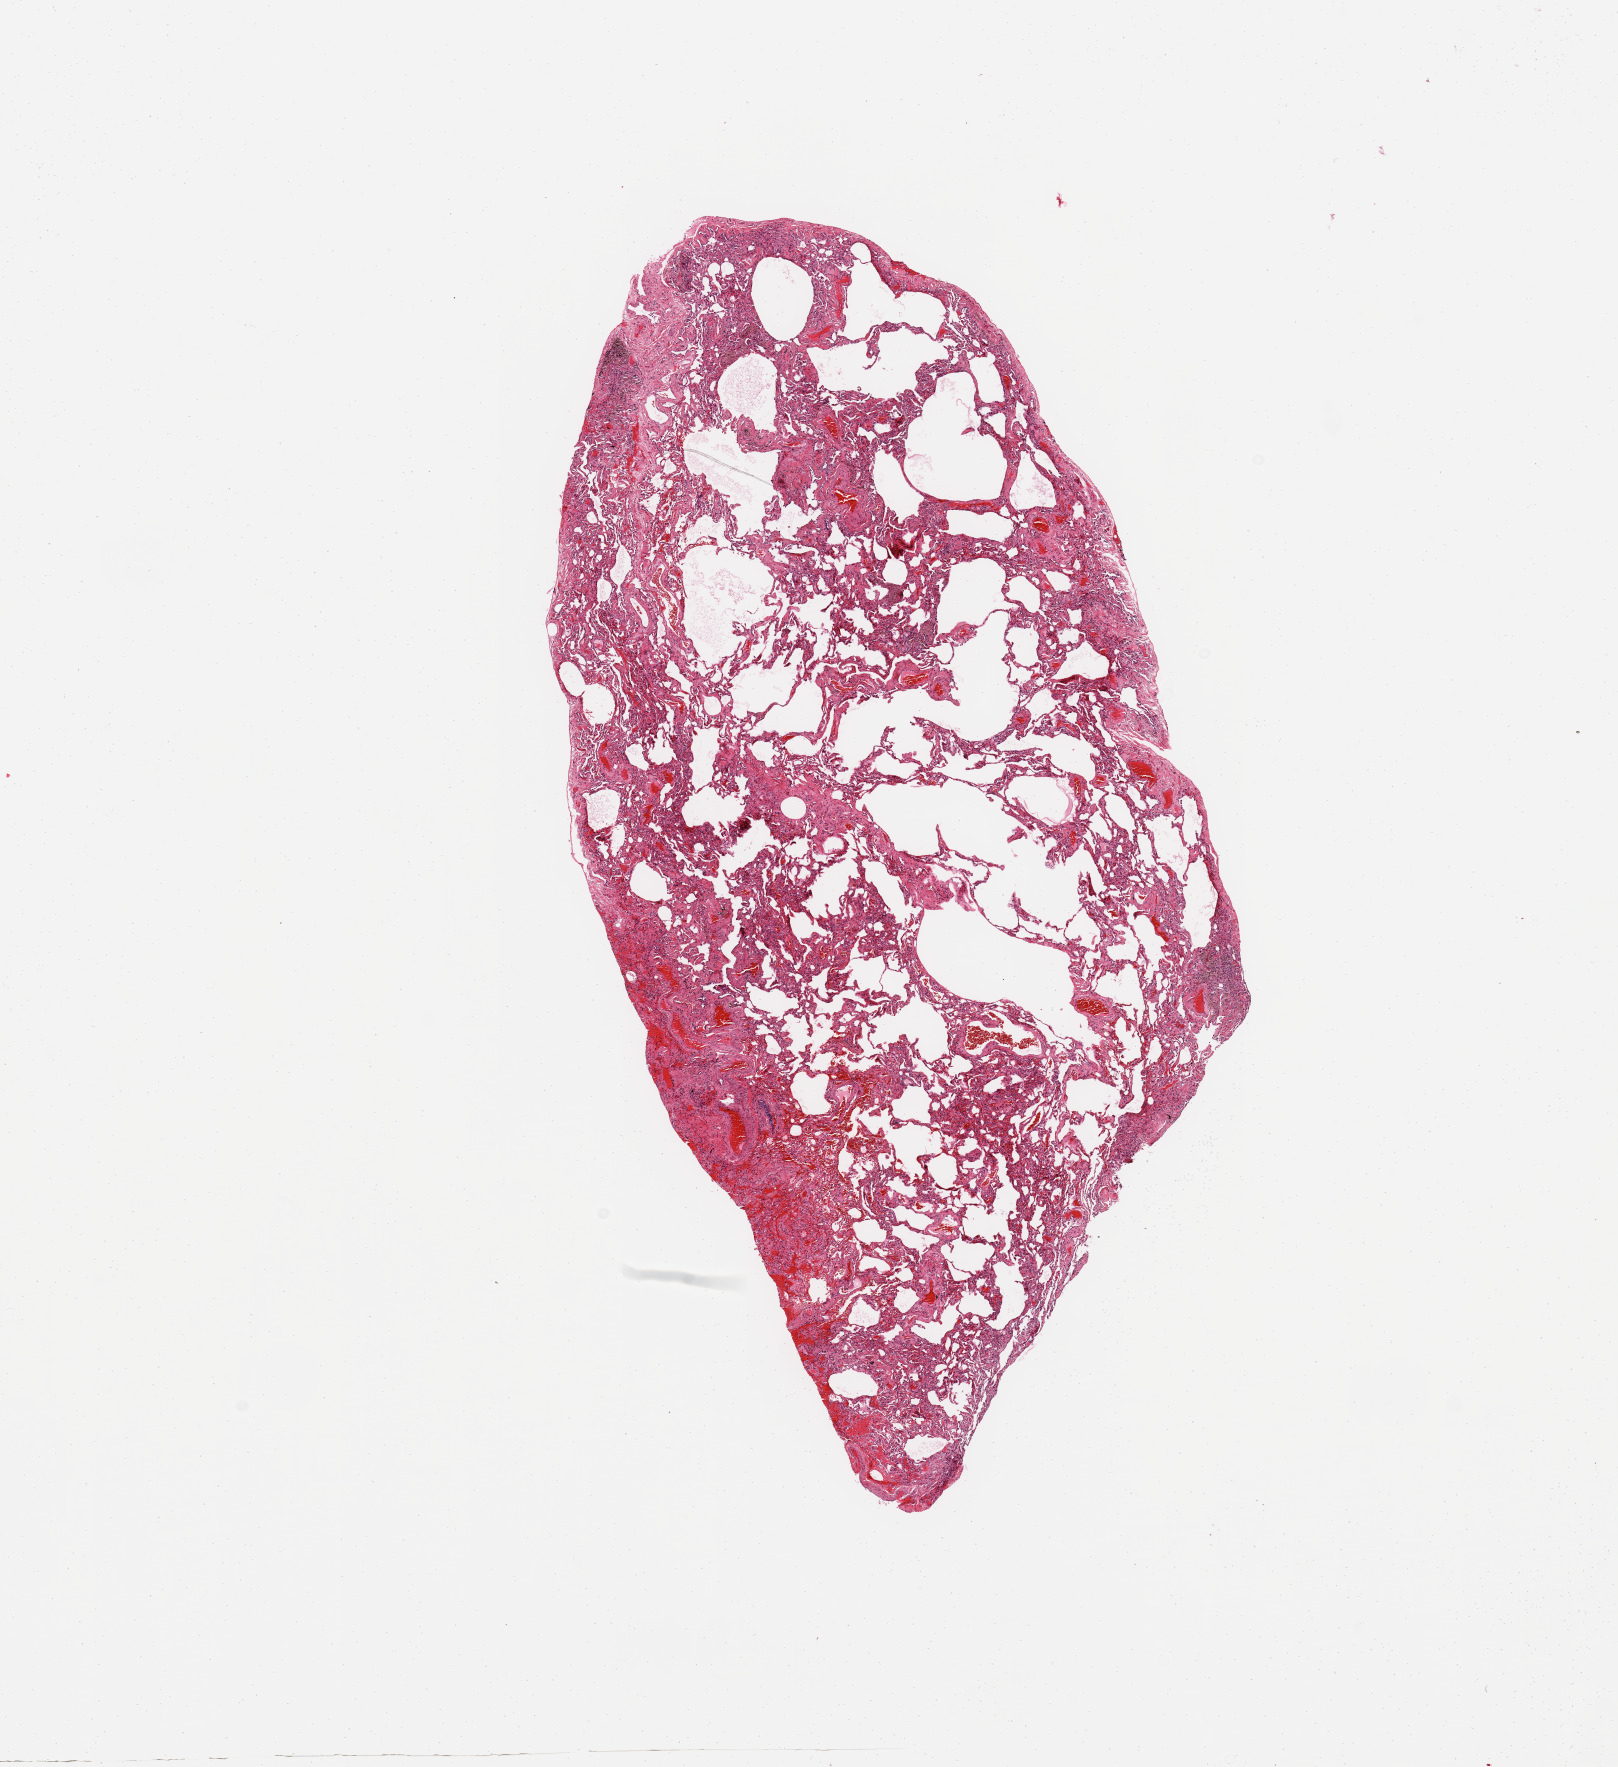
Digitized H&E-stained tissue section (whole slide), whole scanned area (about 12.8 x 14.0 mm) shown as a low-resolution overview. Normal (non-tumour) tissue sample, sampled site: lung. Patient: female, age 58 years.
This section: normal (non-tumour) tissue from the same patient. Patient diagnosis: Adenocarcinoma, NOS.